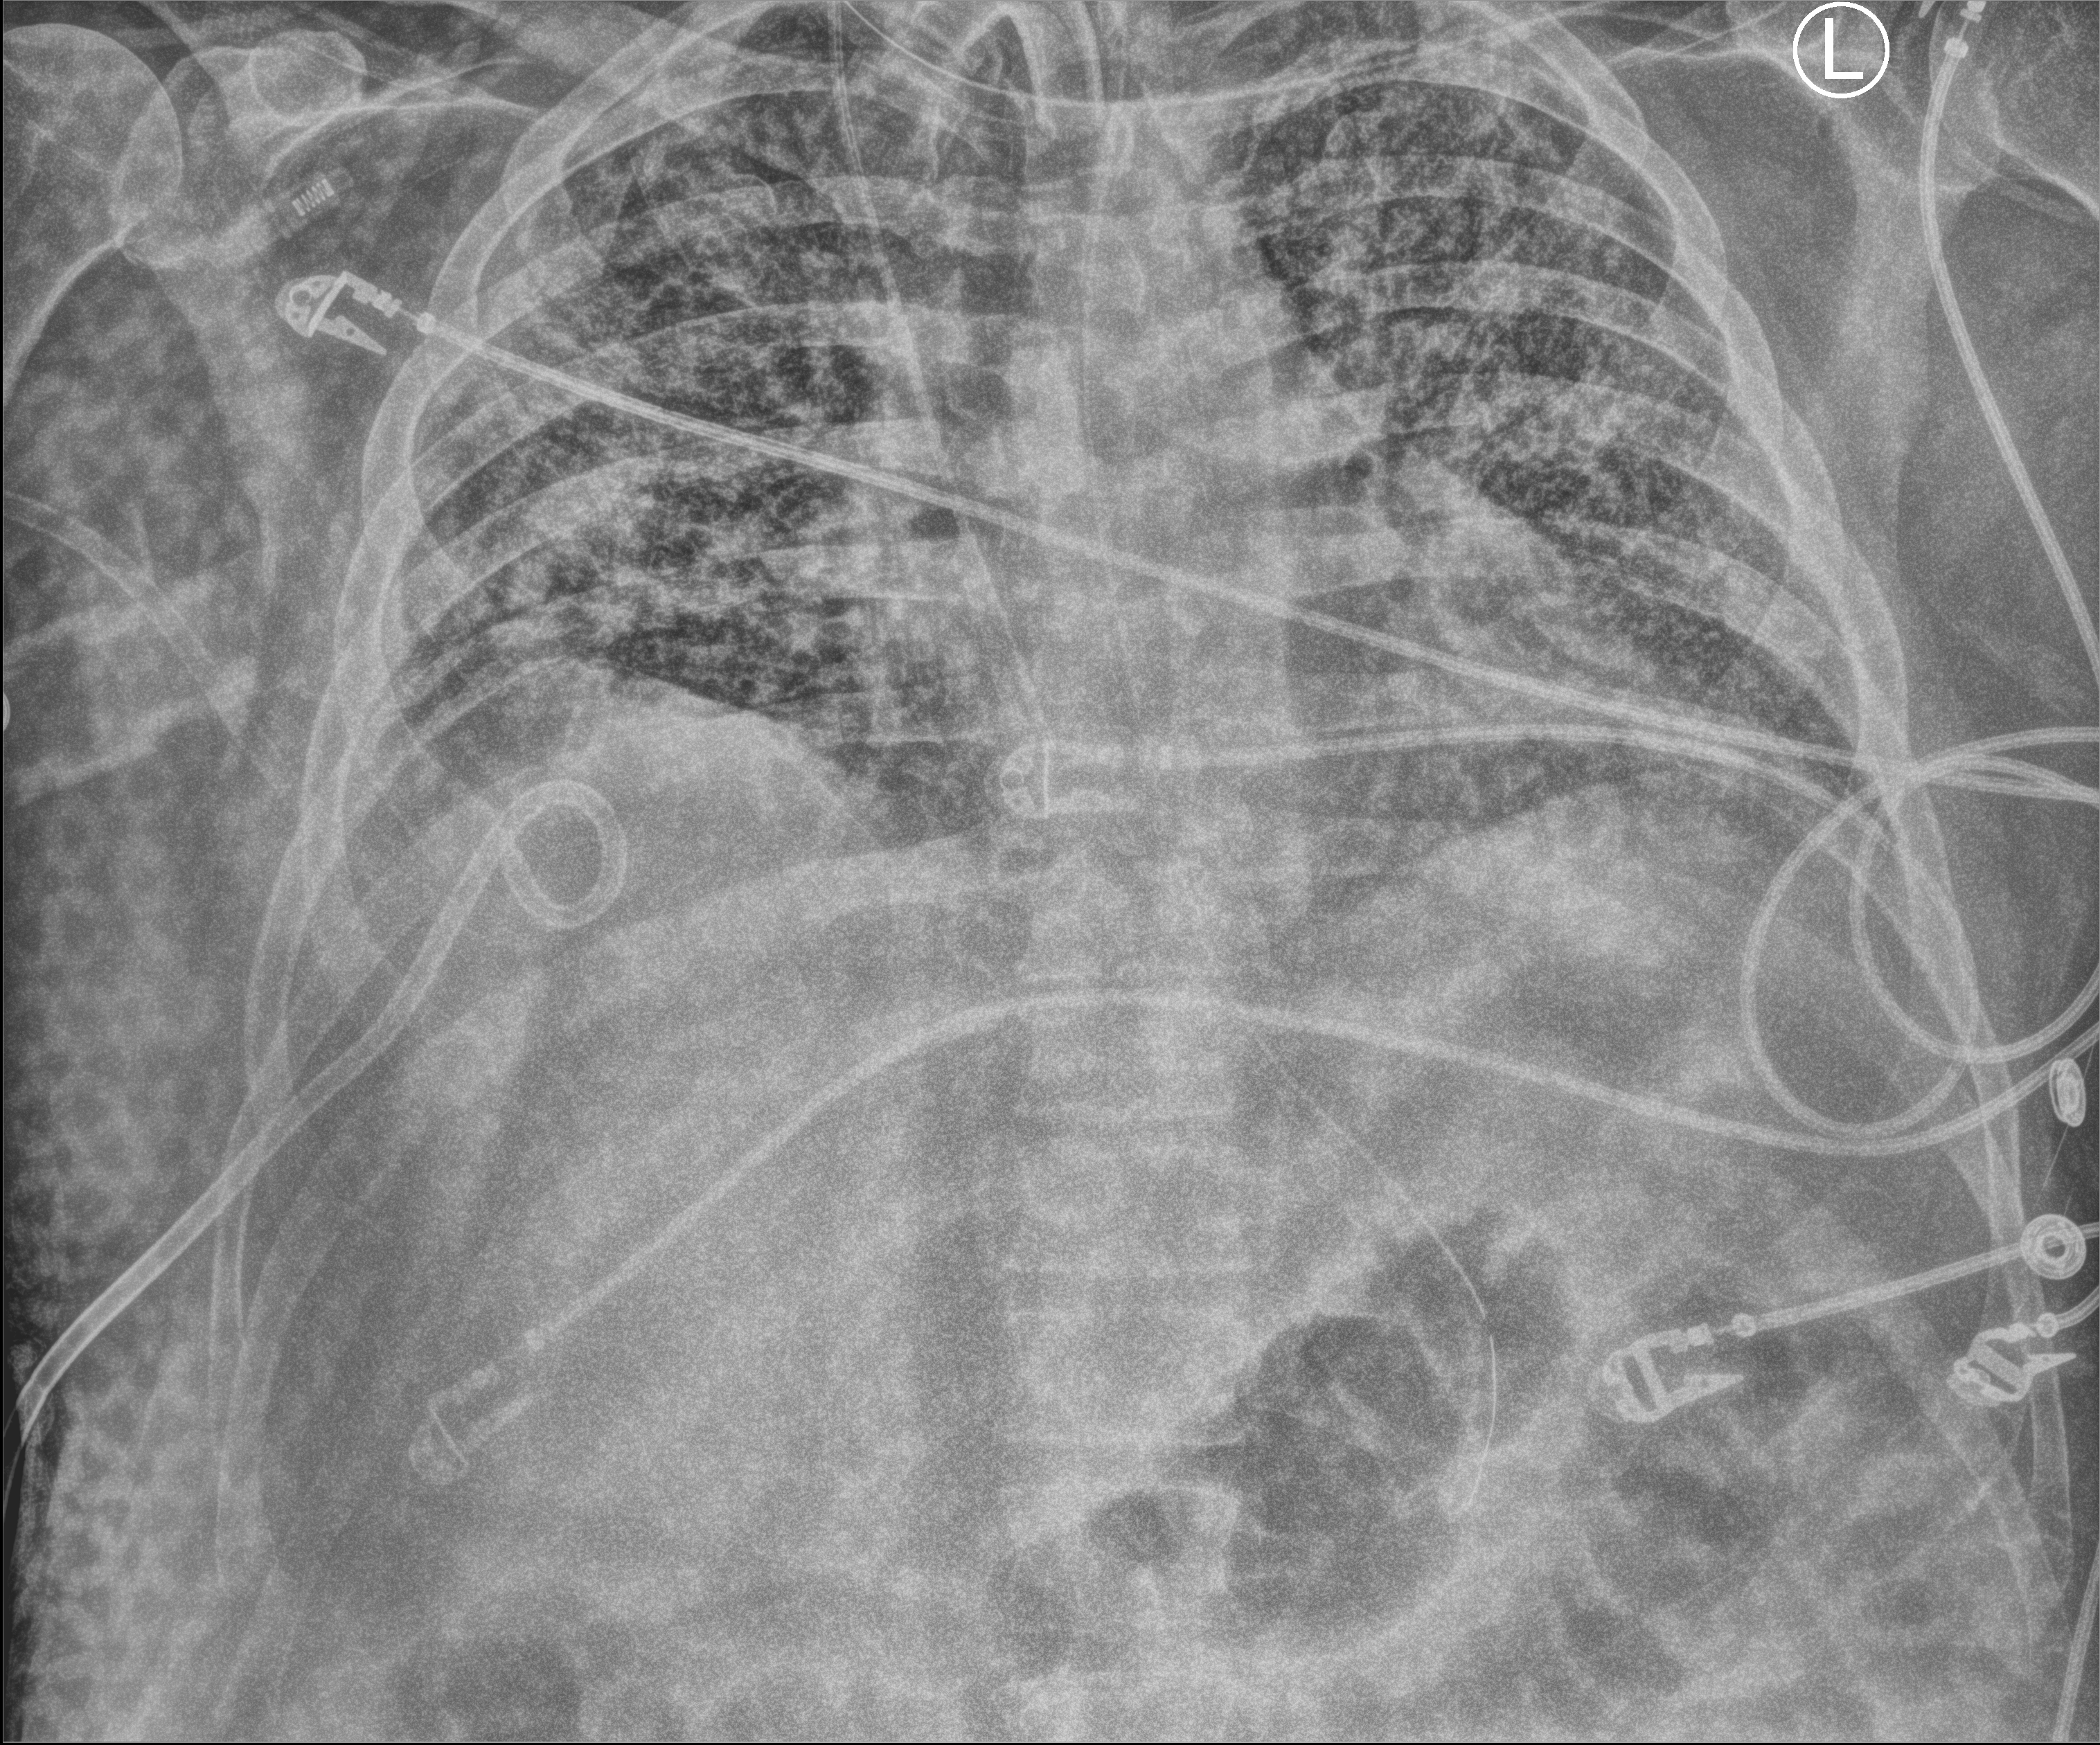
Portable chest radiograph, anteroposterior (AP) projection. Patient hospitalised with COVID-19; male, aged 18–59 years.
Admission-level facts for this patient (not findings on this image; timing relative to this image not recorded):
- mechanically ventilated during this hospital stay: yes